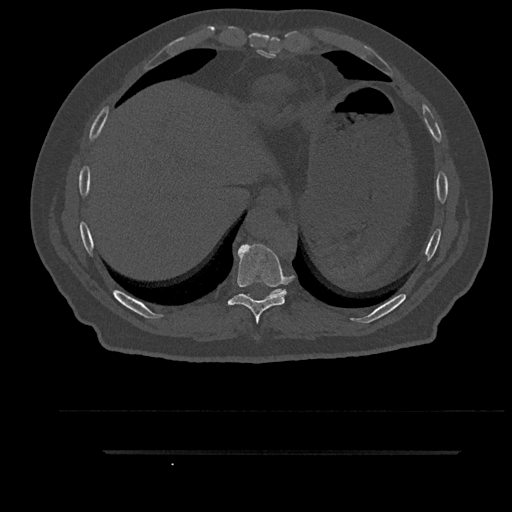
CT including the spine, one axial slice. 120 kVp. Bone window (W 1800 / L 400 HU). 512 × 512 image matrix. Patient: male, 63 years. From the clinical record (not read from this slice): primary cancer: renal.
Structures marked on this image (semi-automatically segmented with operator editing):
- T10 vertebra: box from (x=244, y=289) to (x=284, y=296) px
- T9 vertebra: (x=227, y=244)–(x=294, y=324)